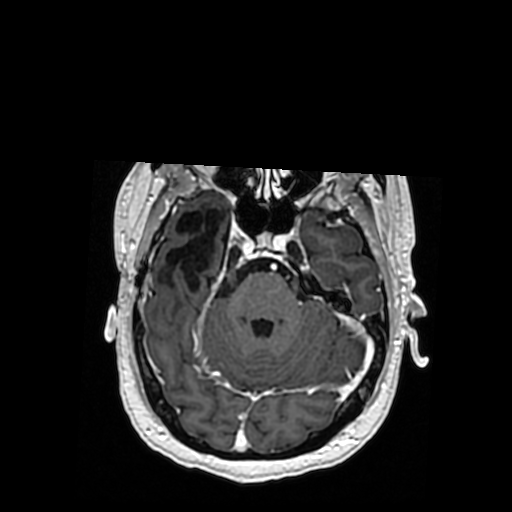
Brain MRI from a brain-tumour surgery series, one axial slice; slice 242 of 364 in the series (ordered by position); T1-weighted post-contrast; 0.5 mm slice thickness; 512 × 512 image matrix, field of view 260 × 260 mm. From the clinical record (not read from this slice): histopathology: Oligodendroglioma; WHO grade: 3; IDH mutation: yes.
Structures marked on this image (manually delineated by an expert):
- previous resection cavity: bounding box [x1, y1, x2, y2] px = [161, 210, 228, 290]